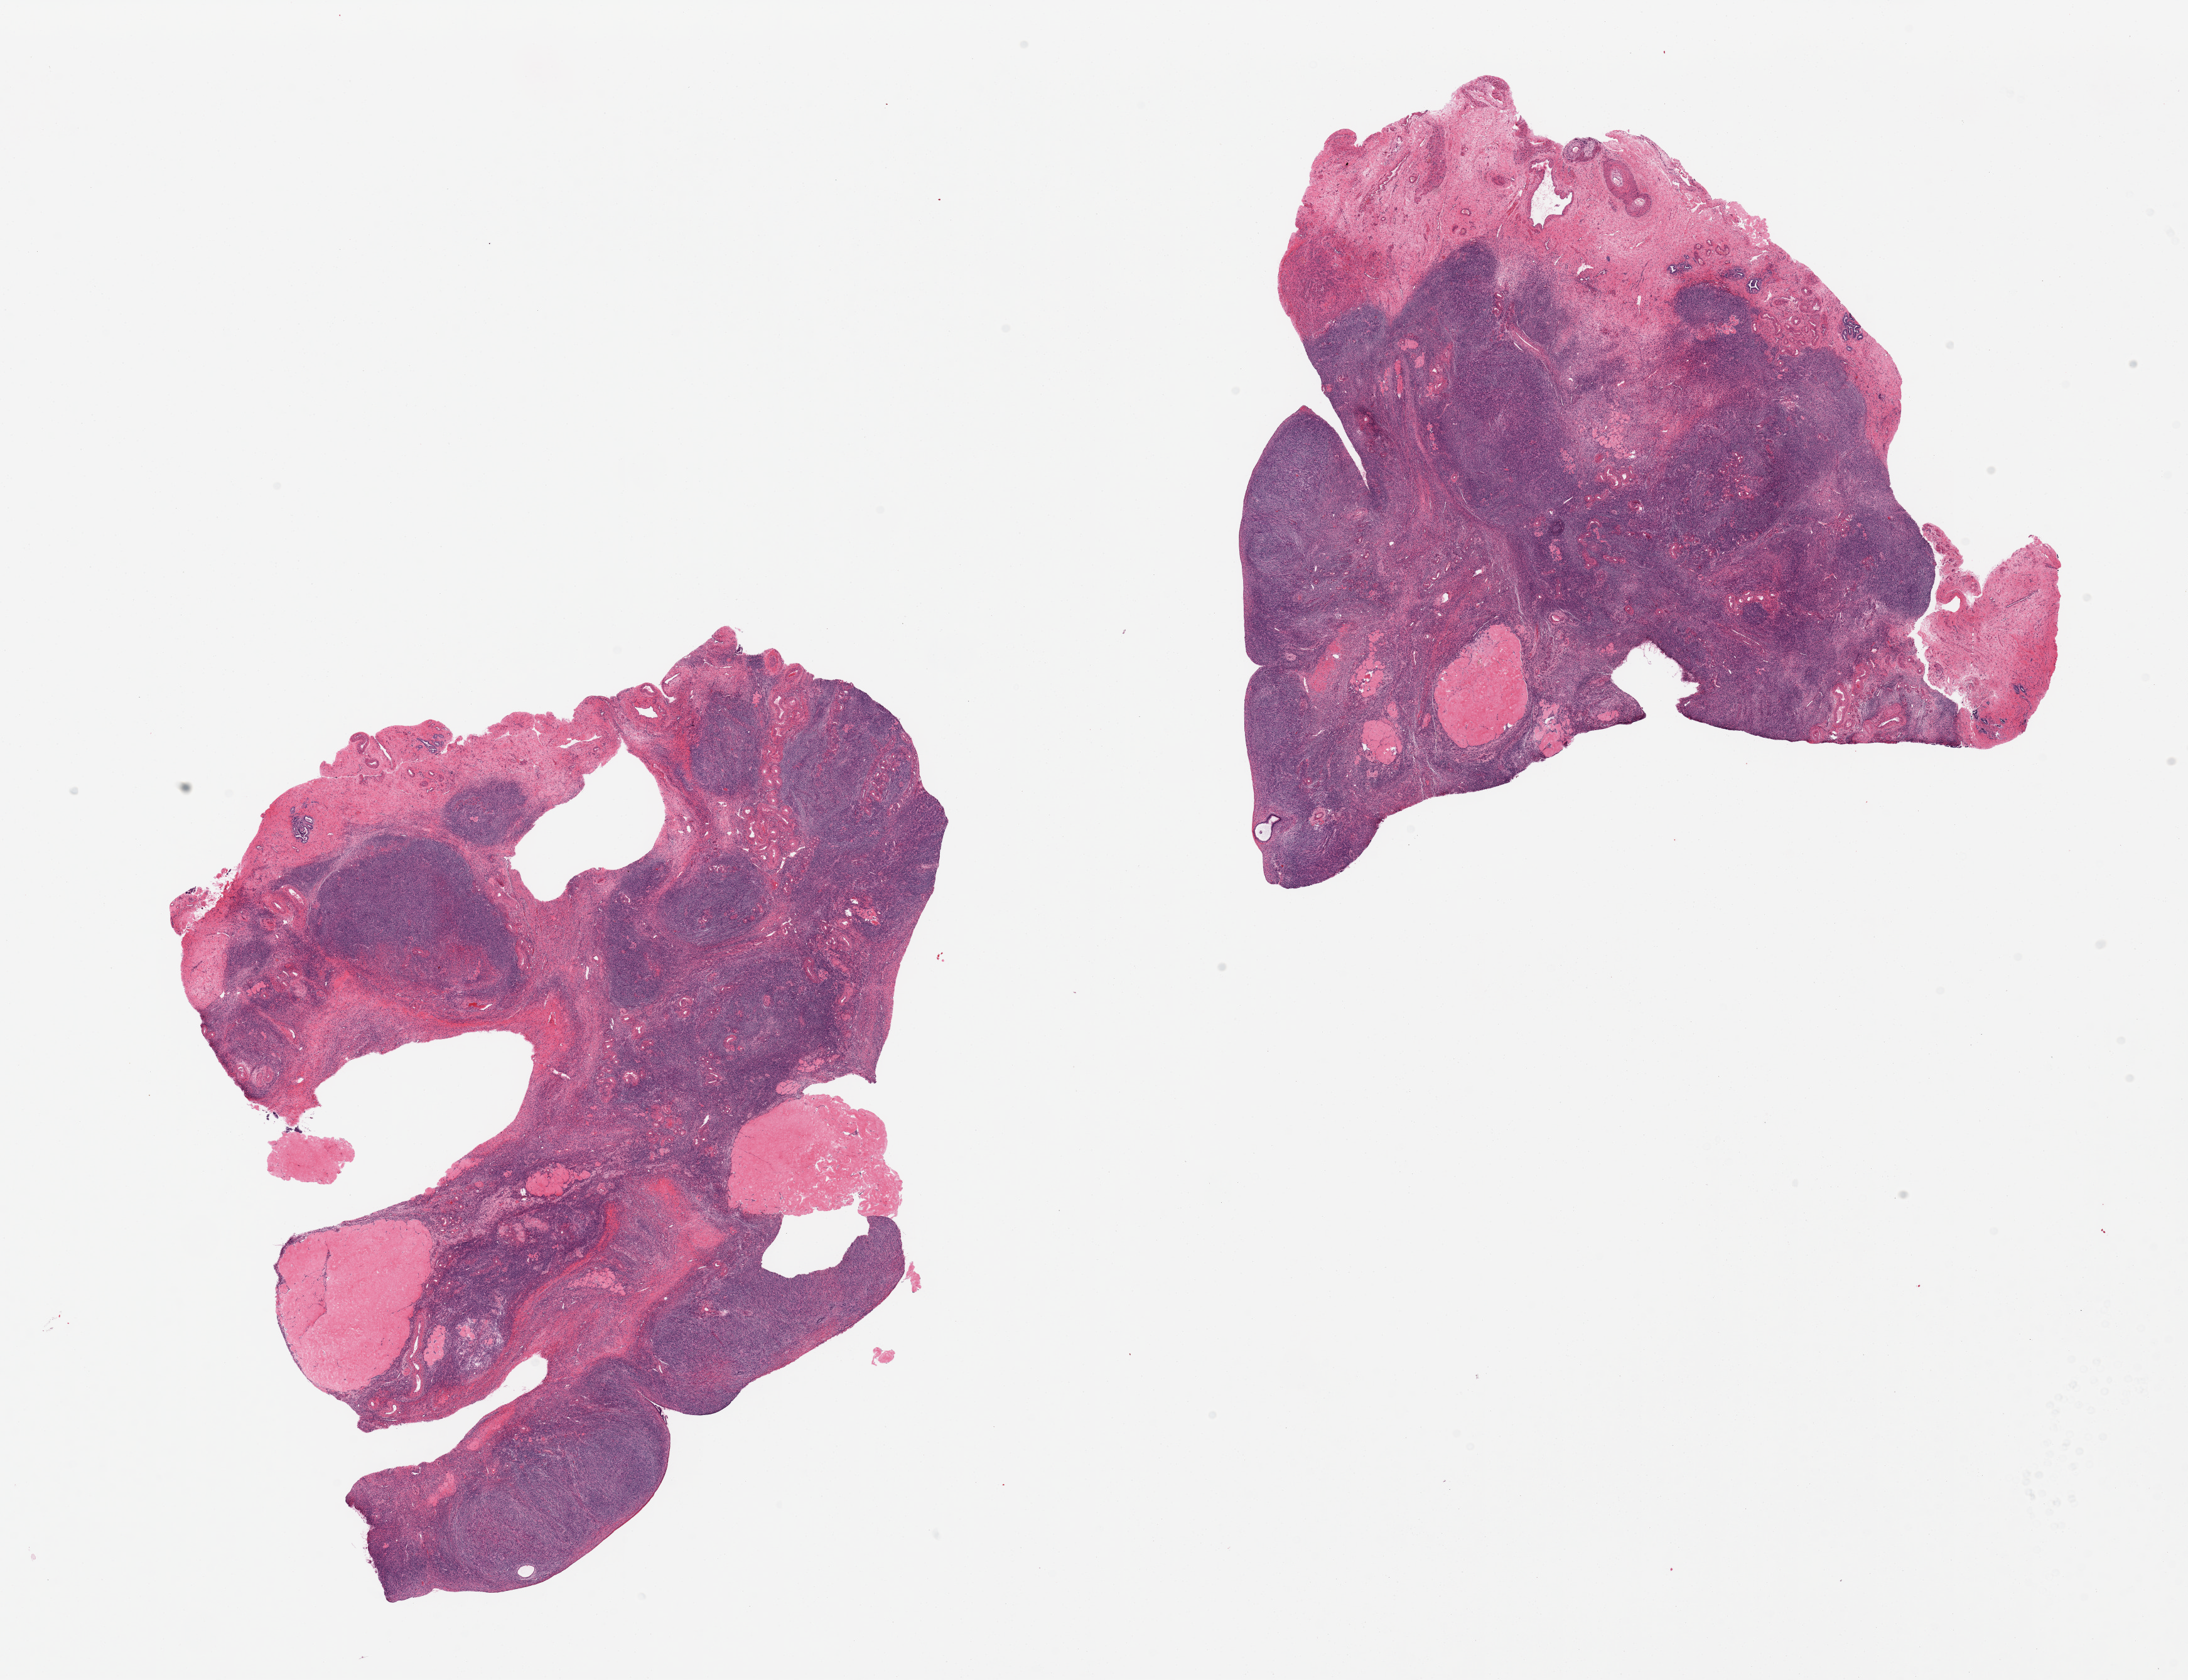
Haematoxylin and eosin whole-slide image, brightfield, shown as a low-resolution overview of the whole scanned area (about 27.6 x 21.2 mm), PAXgene-fixed paraffin-embedded (PFPE) section, sampled site (target tissue): ovary, donor tissue sample. Donor: female.
* review note (as recorded): 2 pieces, typical post menopausal involutional changes